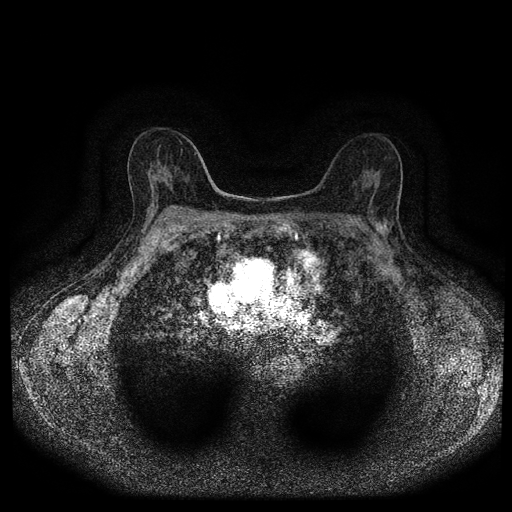
Breast MRI (dynamic contrast-enhanced, multi-phase), one axial slice; slice 58 of 116 in the series (ordered by position); dynamic contrast-enhanced series, time point 2 of 5 at this slice position (early post-contrast); 1.5 T; TE 2.7 ms, TR 5.4 ms; 2 mm slice thickness; 512 × 512 image matrix. Patient: female, 63 years.
Structures marked on this image (semi-automatically segmented with operator editing):
- breast lesion (labelled 'tumour' in the annotation; benign lesions carry a separate 'benign' label): bounding box [x1, y1, x2, y2] px = [373, 218, 391, 238]